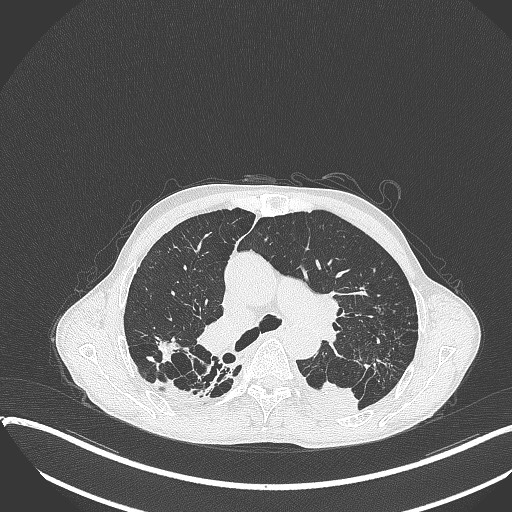
Chest CT, one axial slice; reconstruction kernel B70f; 120 kVp; lung window (W 1500 / L -600 HU); 512 × 512 image matrix. Patient: male, 57 years. Case-level facts recorded for this patient, not image findings: clinical TNM (as recorded): T4 N0 M0.
Outlined on this slice (rectangle marked by the reading radiologist):
- lung tumour (recorded histology: squamous cell carcinoma): box from (x=301, y=374) to (x=361, y=416) px